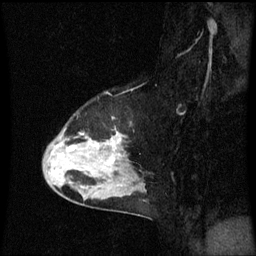
Breast MRI (dynamic contrast-enhanced), one sagittal slice; position 44 of 60 along the scan axis; dynamic contrast-enhanced series, image 2 of 3 at this slice position (ordered by acquisition); 1.5 T; TE 4.2 ms, TR 8.9 ms; 2 mm slice thickness; 256 × 256 image matrix, field of view 200 × 200 mm. Female patient, age 50 years. Case-level facts recorded for this patient, not image findings: setting: breast cancer imaged before/during neoadjuvant chemotherapy; receptor status: HR-positive, HER2-negative.
Structures marked on this image (semi-automatically segmented with operator editing):
- analysis volume of interest (the breast-tissue region the enhancement analysis was run in; not a lesion): box from (x=45, y=134) to (x=147, y=205) px
- tumour enhancement mask (voxels above the 70 % enhancement threshold inside the analysis volume of interest): (x=68, y=142)–(x=115, y=165)